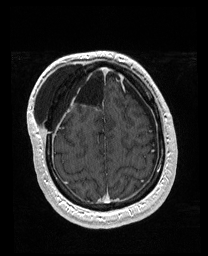
Brain MRI from a brain-tumour surgery series, one axial slice. Position 48 of 176 along the scan axis. T1-weighted post-contrast. 208 × 256 image matrix, field of view 208 × 256 mm. From the clinical record (not read from this slice): histopathology: Astrocytoma; WHO grade: 4; IDH mutation: yes.
Structures marked on this image (manually delineated by an expert):
- previous resection cavity: bounding box [x1, y1, x2, y2] px = [56, 65, 106, 106]